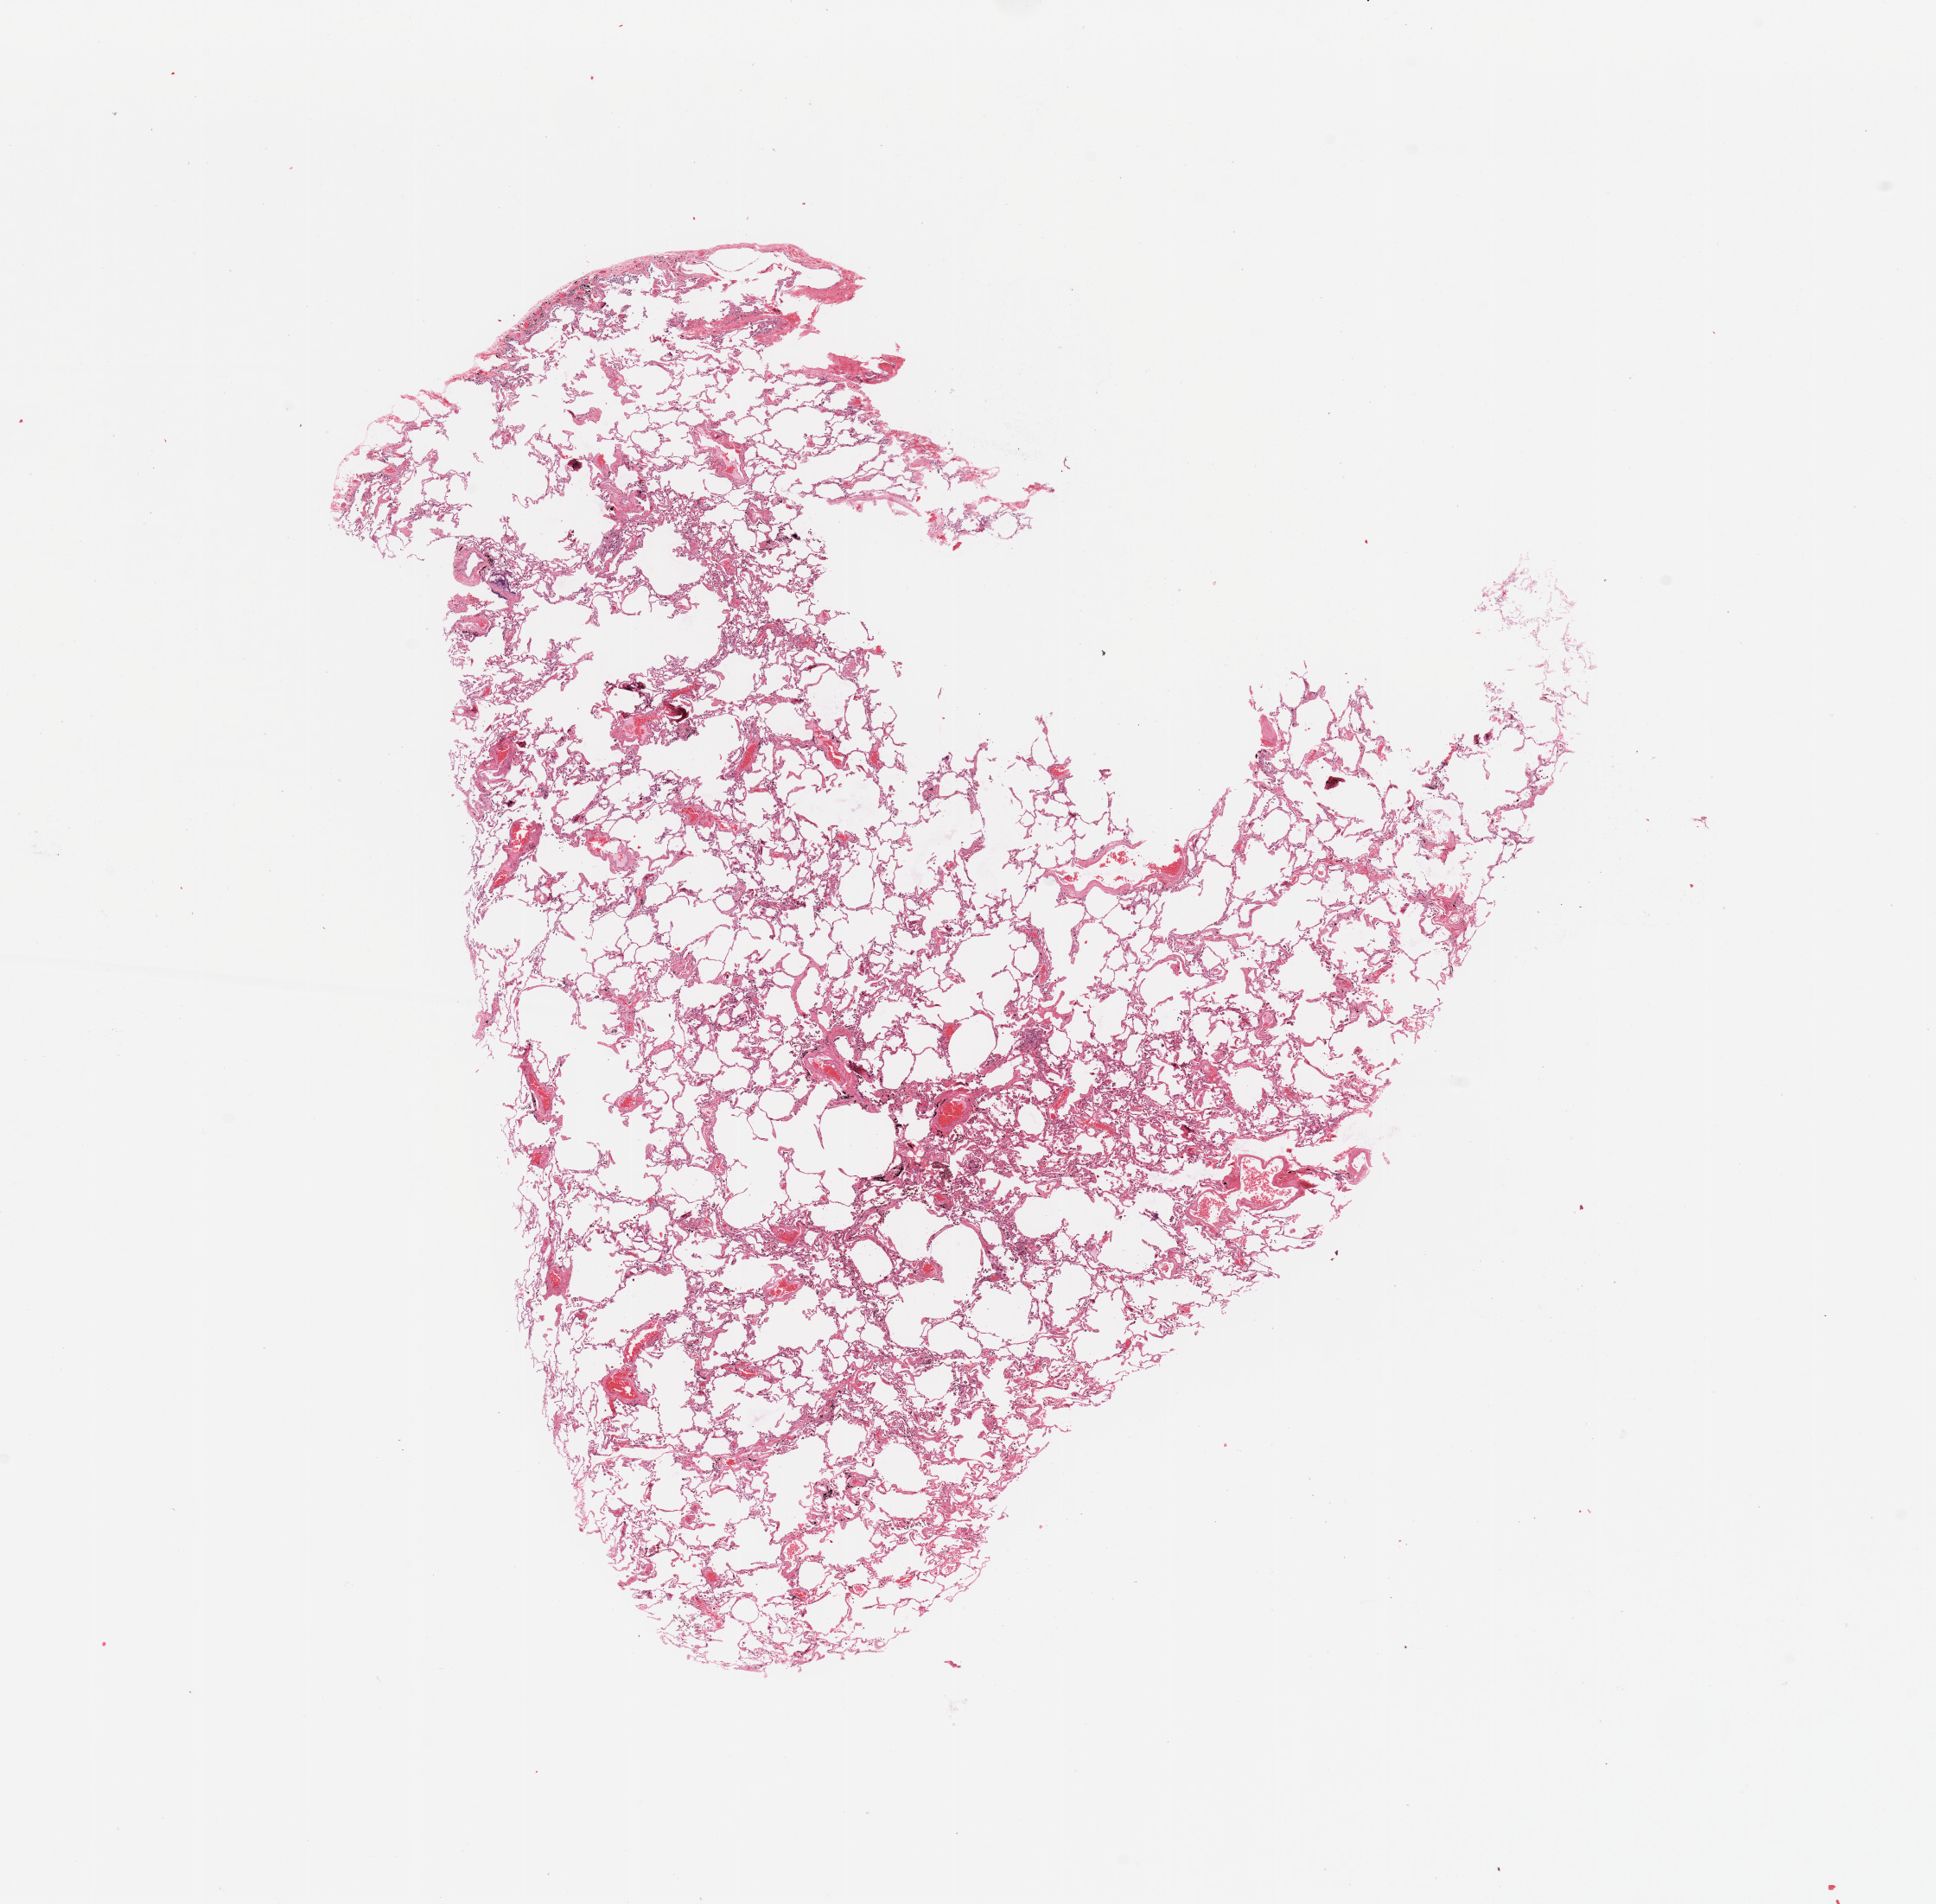
Whole-slide histology image, H&E, shown as a low-resolution overview of the whole scanned area (about 17.7 x 17.4 mm, slide scanned at 20x); normal (non-tumour) tissue sample, sampled site: lung. Male, 62 y/o.
This section: normal (non-tumour) tissue from the same patient. Patient diagnosis: Adenocarcinoma, NOS.